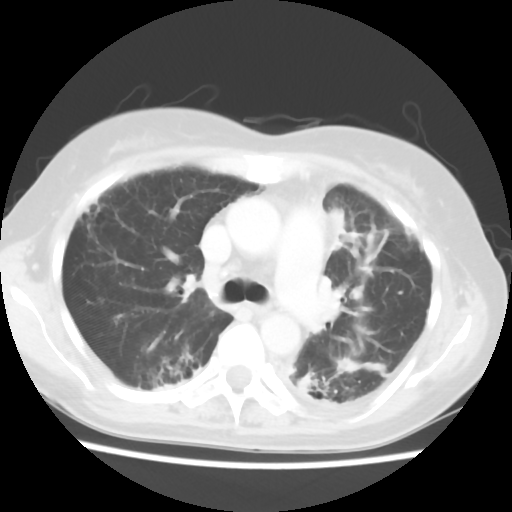
Chest CT, one axial slice; slice 37 of 56 in the series (ordered by position); reconstruction kernel STANDARD; 120 kVp; lung window (W 1500 / L -600 HU); 512 × 512 image matrix, field of view 309 × 309 mm. Female patient, age 56 years. Case-level facts recorded for this patient, not image findings: clinical TNM (as recorded): T1c N0 M1.
Outlined on this slice (bounding box drawn by a radiologist):
- lung tumour (recorded histology: adenocarcinoma): bounding box [x1, y1, x2, y2] px = [325, 202, 350, 251]